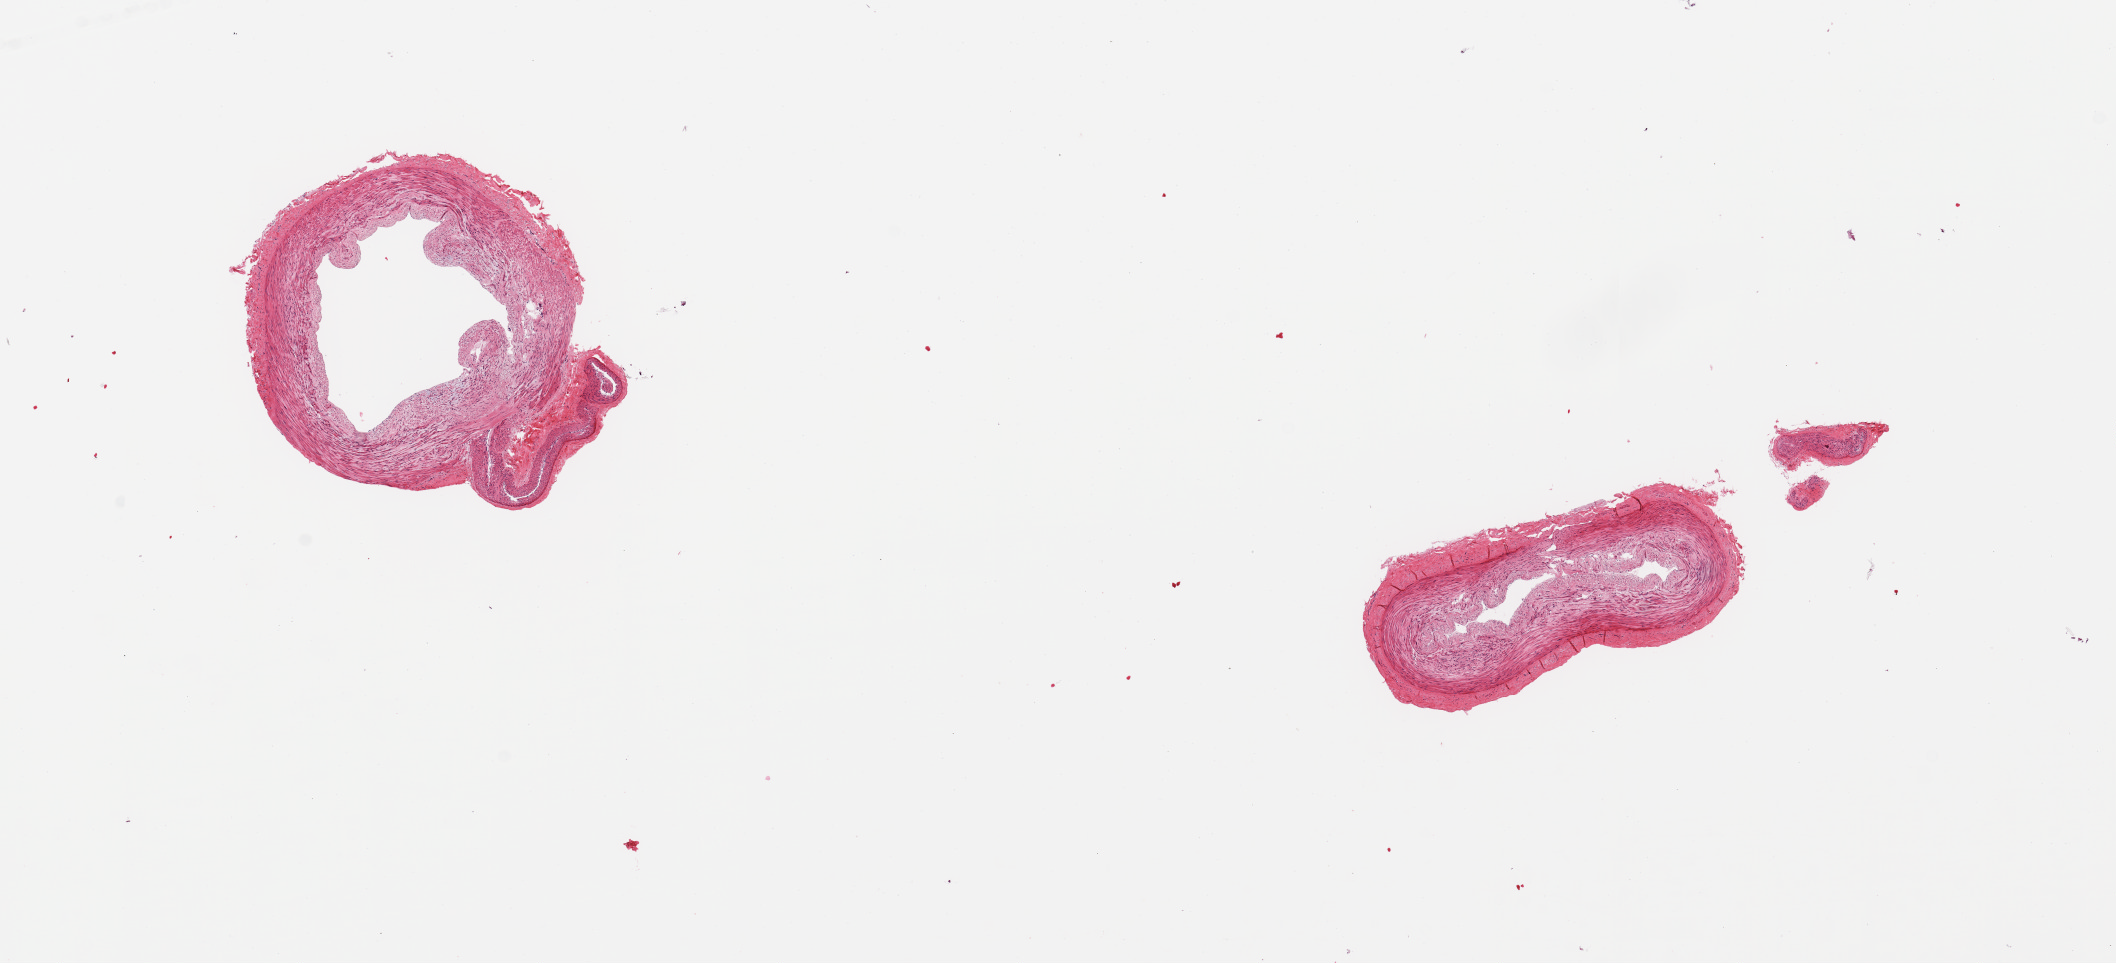
Digitized haematoxylin and eosin-stained section, whole scanned area (about 16.7 x 7.6 mm) shown as a low-resolution overview, PAXgene-fixed, paraffin-embedded tissue, sampled site (target tissue): tibial artery, donor tissue sample. Donor: male.
• pathologist's review note for this sample: 2 pieces, no adherent fat, no significant atherosis